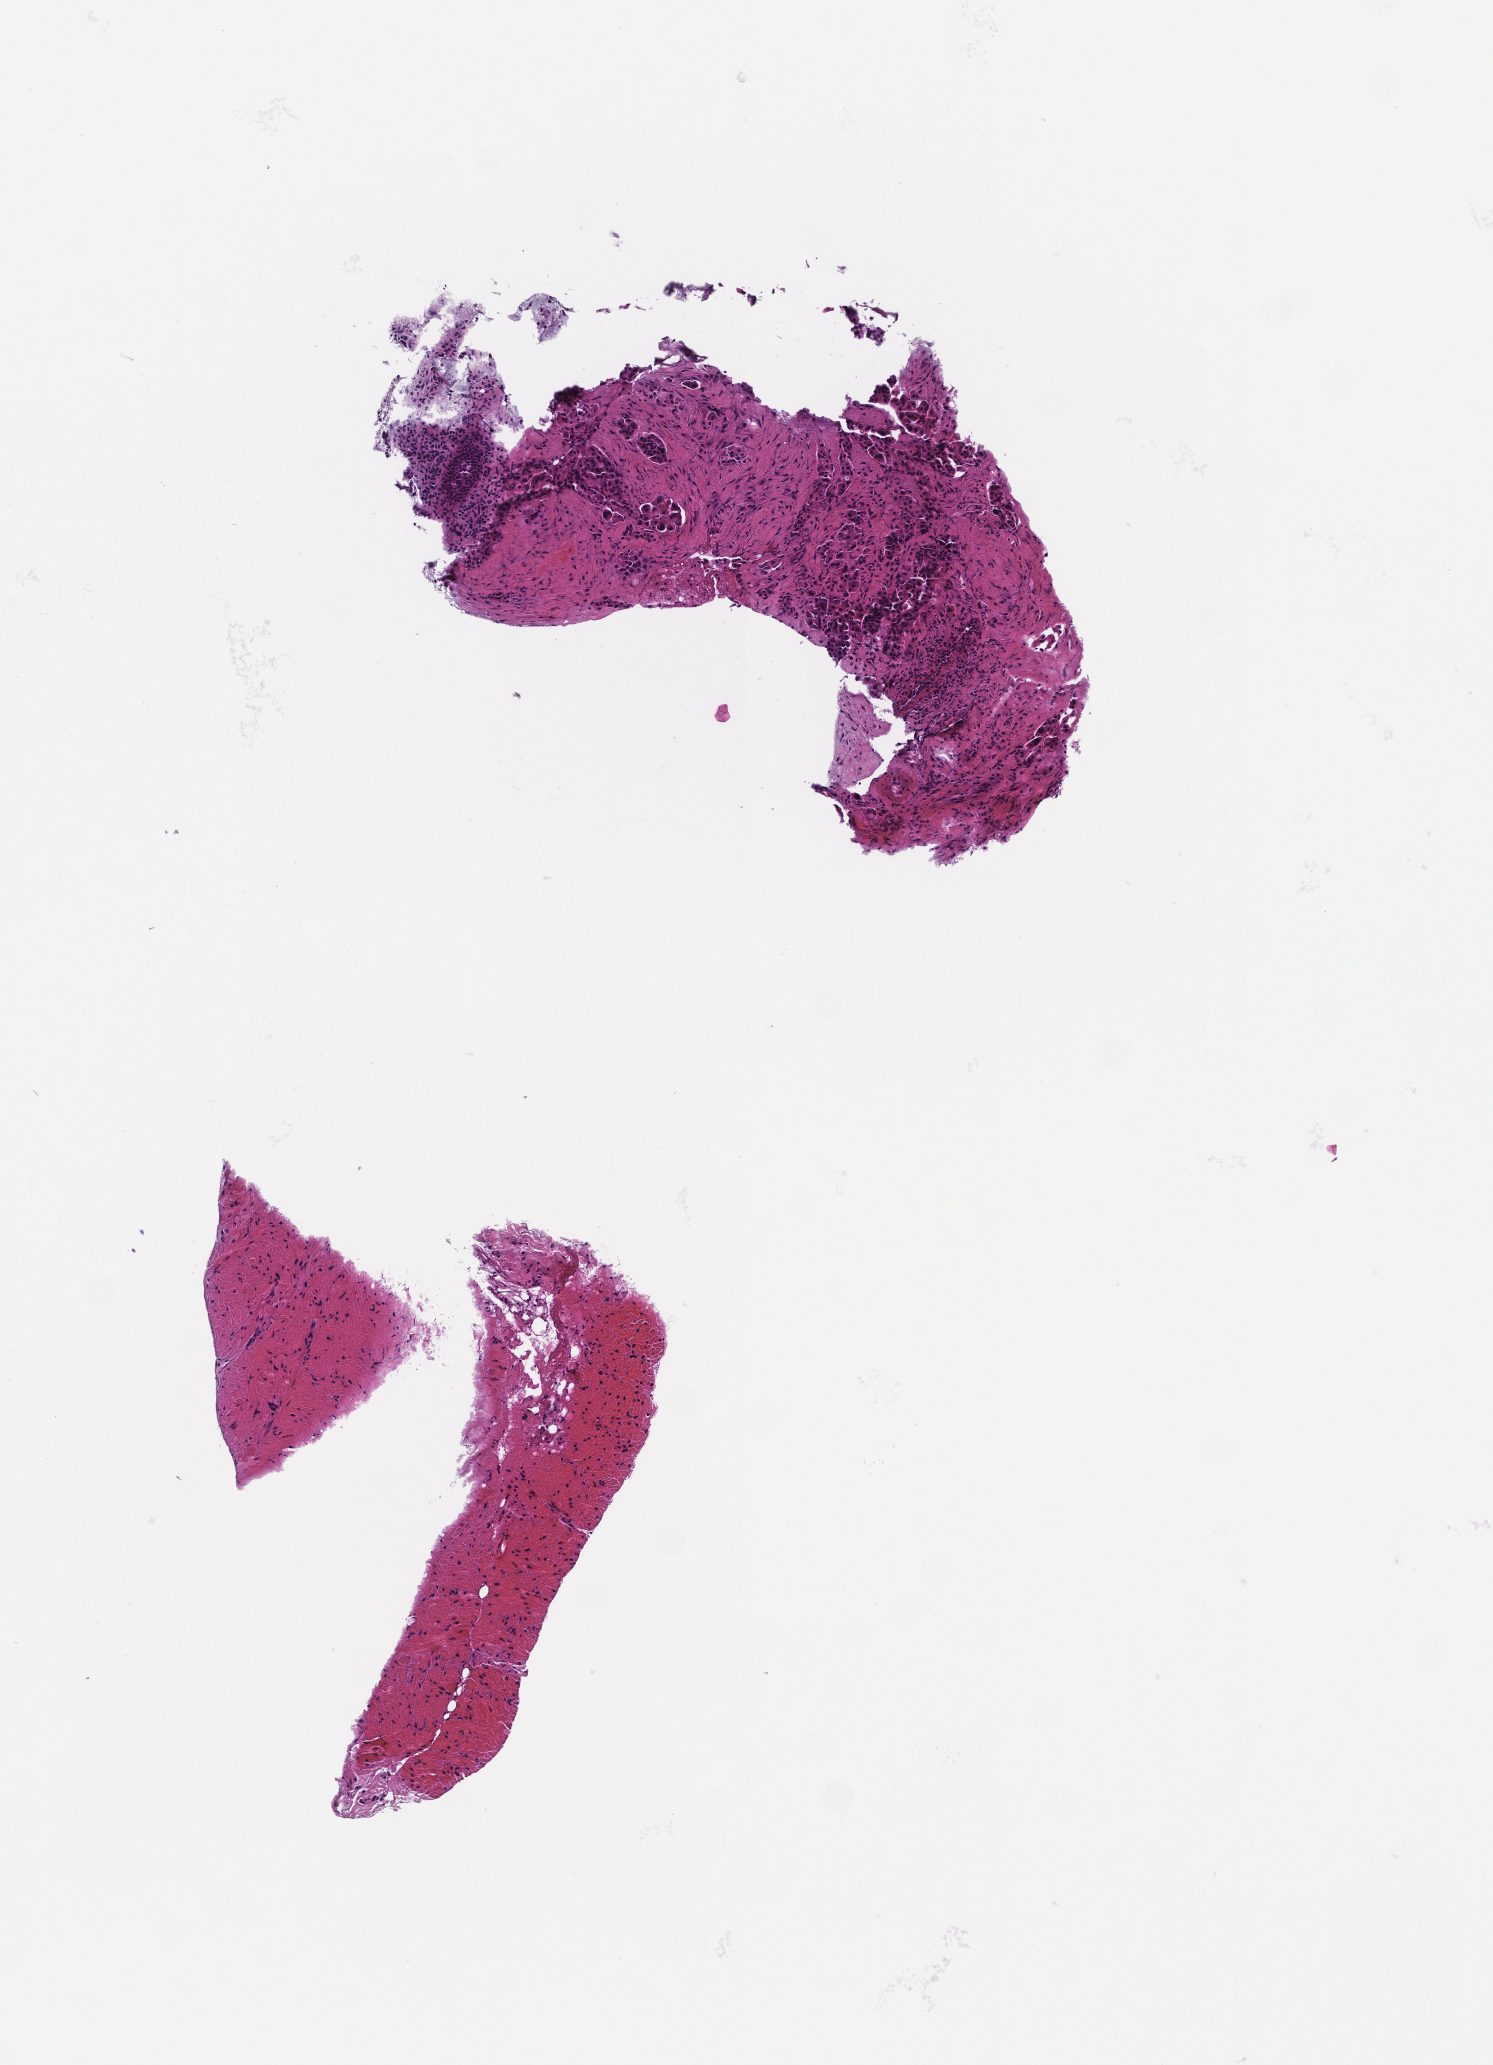
Digitized haematoxylin and eosin-stained section, a low-resolution overview of the entire scanned area, about 3.0 x 4.2 mm, paraffin-embedded section, collected at baseline (before treatment). Patient sex: female.
This section: metastasis (sampled organ not recorded). Patient diagnosis (primary): Ovarian Carcinoma.